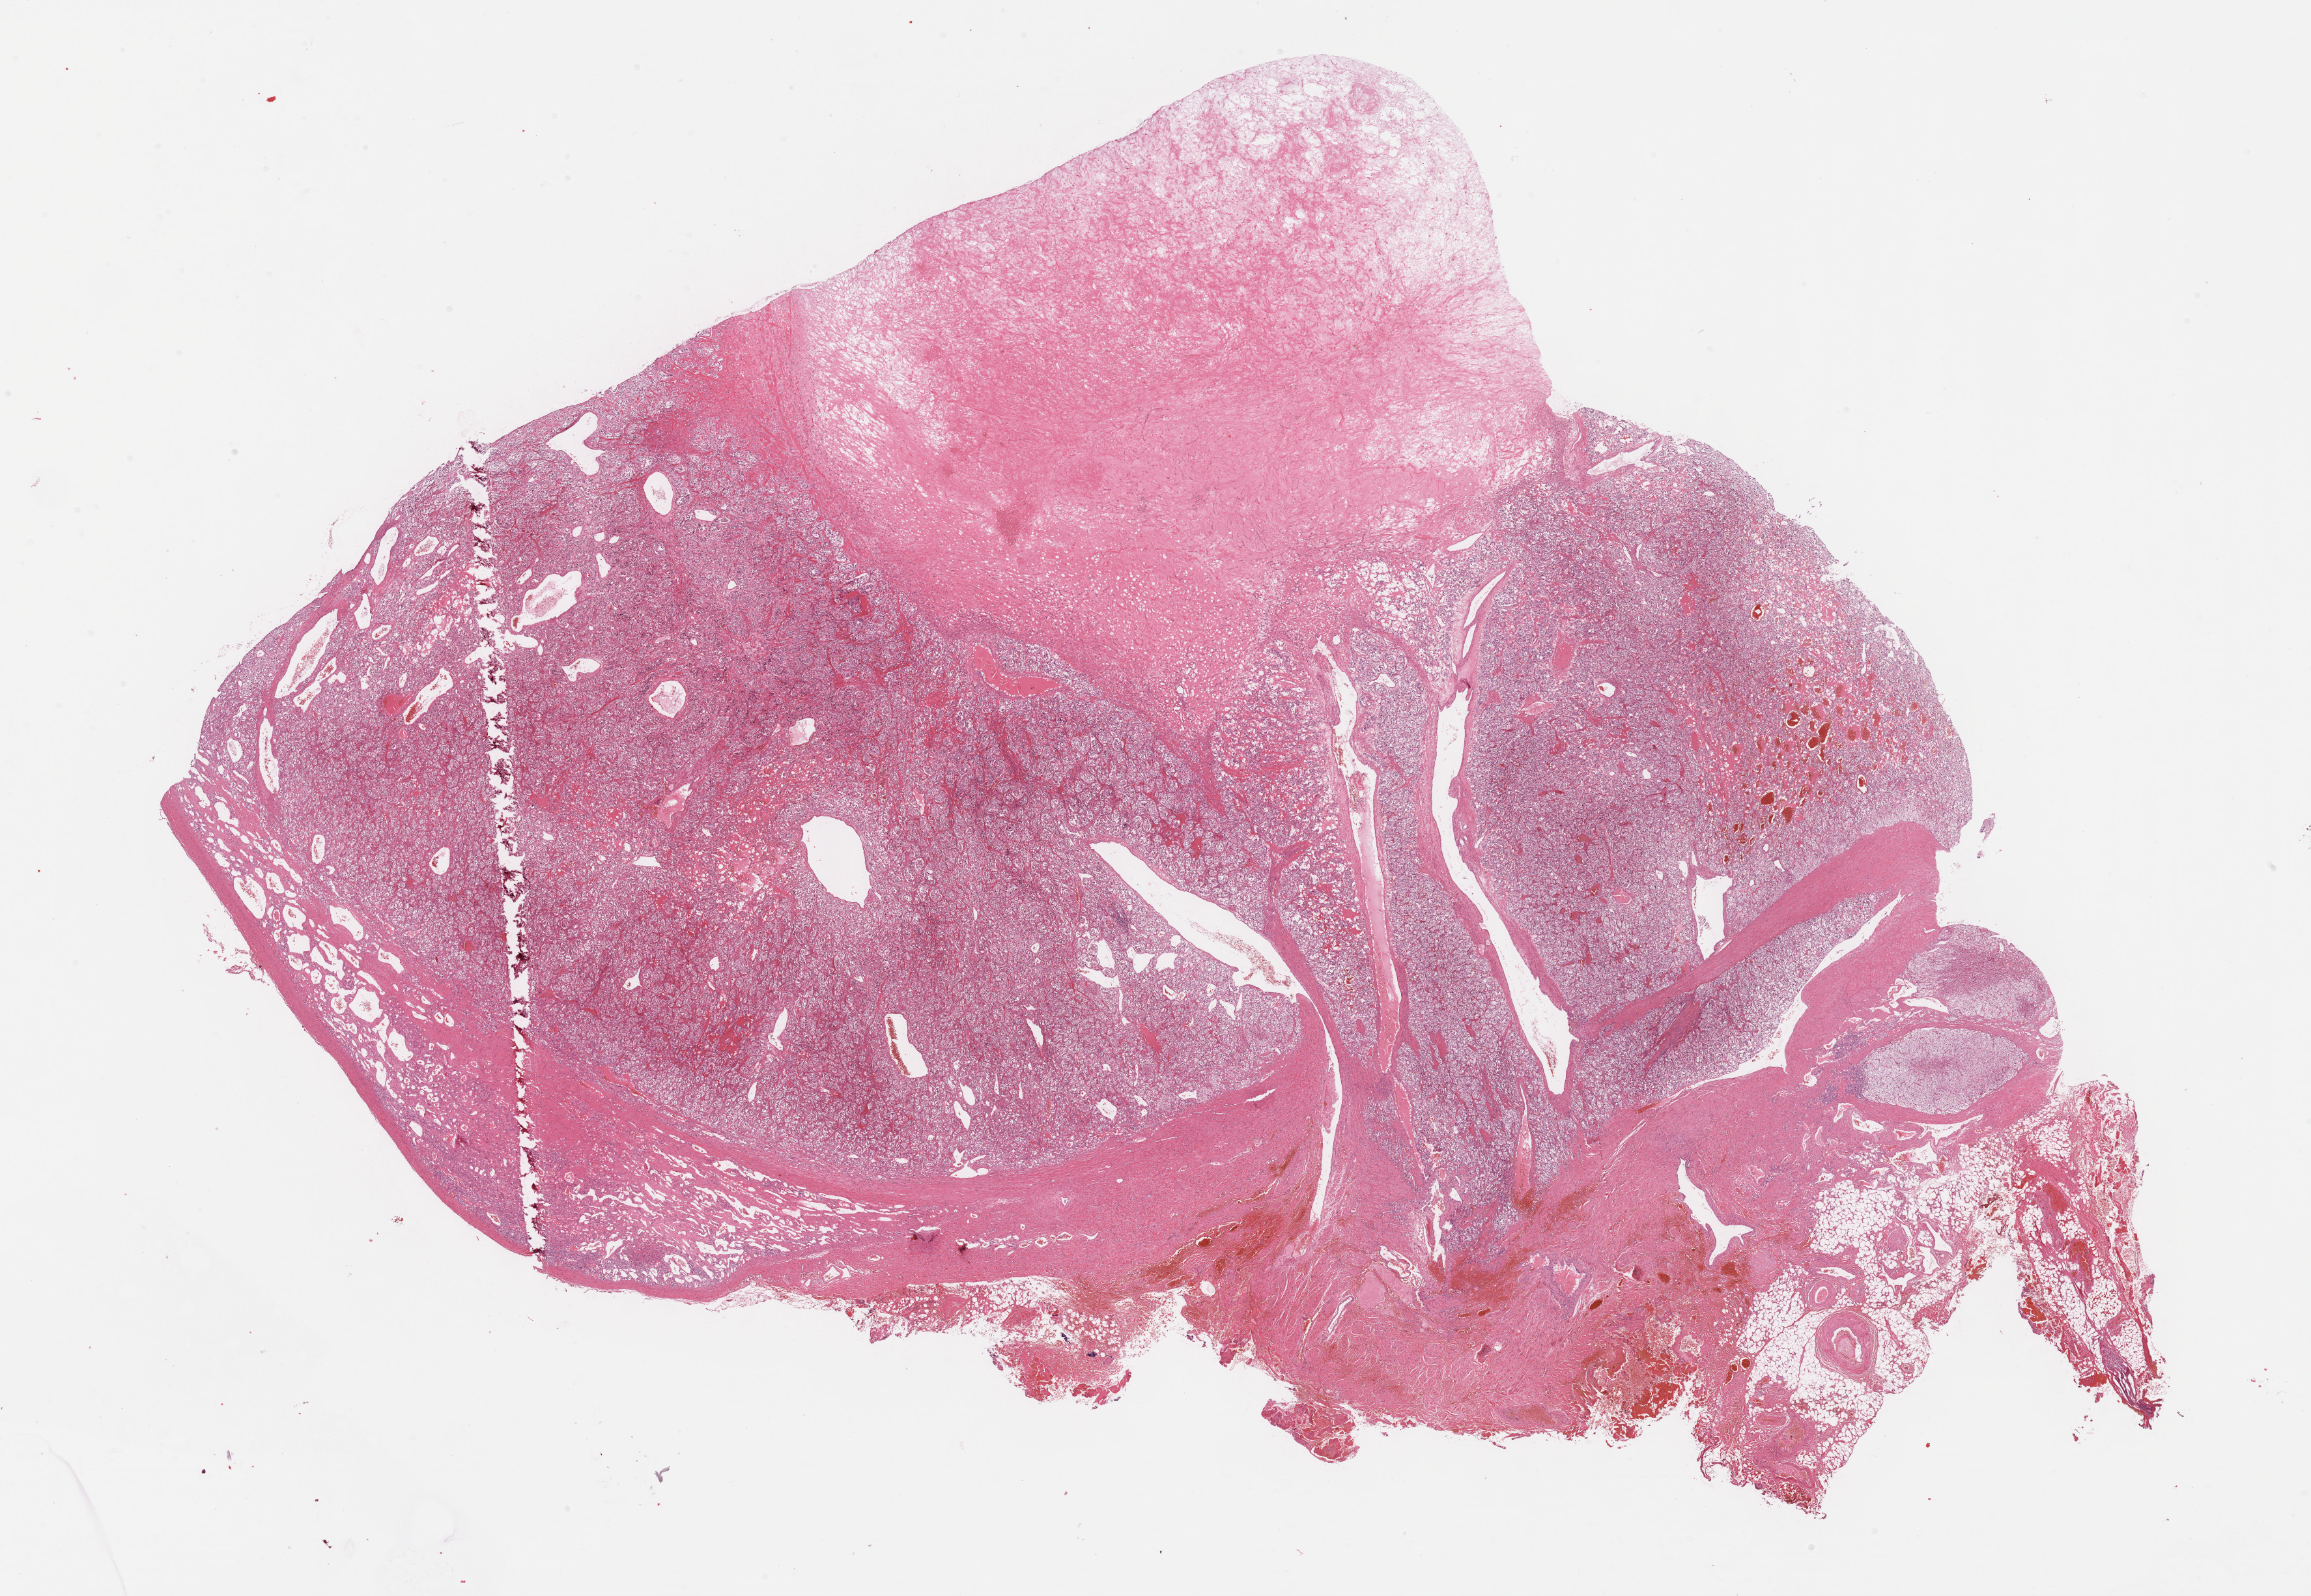
Hematoxylin and eosin (H&E) stained whole-slide image, a low-resolution overview of the entire scanned area, about 28.7 x 19.8 mm (acquisition: 40x scan); formalin-fixed paraffin-embedded (FFPE) diagnostic section; sample: primary tumour, adrenal gland. Male, age 23 years at initial diagnosis.
Histologic diagnosis: Clear cell carcinoma (kidney, NOS).